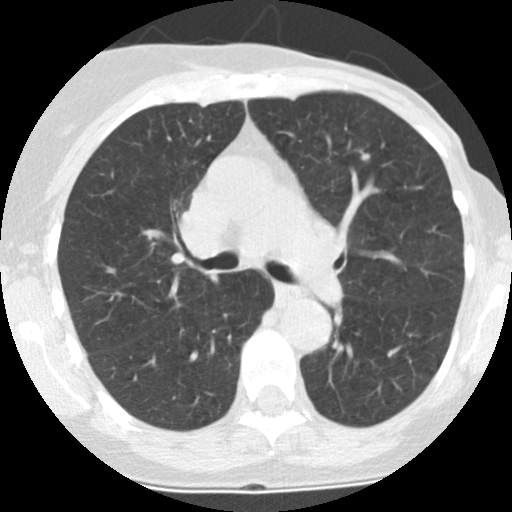
Chest CT (low-dose screening protocol), one axial image; baseline screening round; lung window (W 1500 / L -600 HU); 120 kVp; 512 × 512 image matrix. Female, age 66 years at enrolment. Former smoker at enrolment.
• Lesion marked by an expert reader, bounding box [x1, y1, x2, y2] px = [358, 147, 374, 167].
• No non-calcified nodule or mass ≥4 mm was recorded by the screening reader at this exam.
• Official screen result: negative screen, minor abnormalities not suspicious for lung cancer.
• Participant outcome: lung cancer diagnosed 583 days after this screen — adenocarcinoma, NOS, left lower lobe, poorly differentiated (G3), stage IA (AJCC 6th edition), 8 mm at pathology.